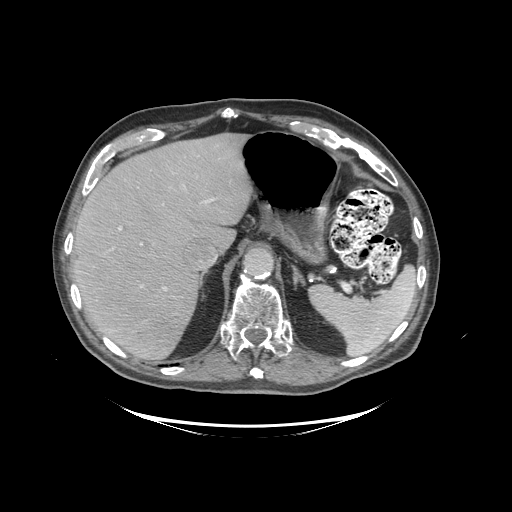
Contrast-enhanced abdominal CT (liver protocol), one axial slice; position 71 of 99 along the scan axis; reconstruction kernel STANDARD; 140 kVp; soft-tissue window (W 400 / L 40 HU); 2.5 mm slice thickness; 512 × 512 image matrix, field of view 460 × 460 mm. Case-level facts recorded for this patient, not image findings: diagnosis: hepatocellular carcinoma (patient treated with transarterial chemoembolisation; whether this scan precedes or follows treatment is not stated here); TNM stage (as recorded): Stage-I; Child-Pugh class: A.
Annotated regions visible in this slice (semi-automatic segmentation, software-assisted and operator-edited):
- liver parenchyma outside the tumour (the mass and vessels are separate outlines, so this box may not span the whole liver): box from (x=72, y=133) to (x=252, y=360) px
- liver vessels: (x=118, y=186)–(x=213, y=290)